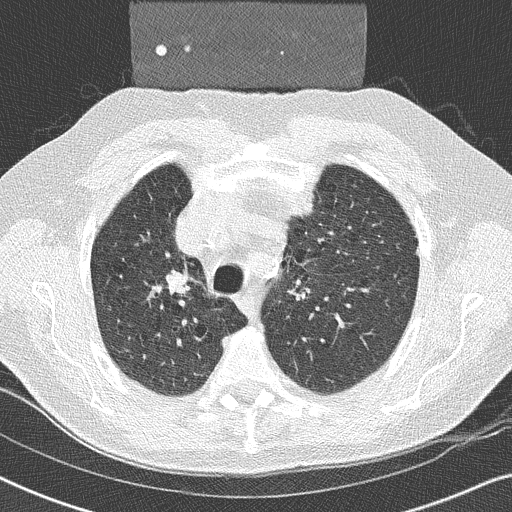
Chest CT (low-dose screening protocol), one axial image. Second annual screen. Lung window (W 1500 / L -600 HU). 2 mm slice thickness. Slice 71 of 252 in the series. Male, age 59 years at enrolment. Former smoker at enrolment.
• Expert-annotated lung lesion, bounding box [x1, y1, x2, y2] px = [151, 259, 207, 308].
• The exam's reader record, not a measurement of the box and not confirmed to be the same lesion: non-calcified nodule or mass ≥4 mm, right upper lobe, 17 × 16 mm, smooth margins, soft tissue attenuation, pre-existing on the prior screen: yes.
• Official screen result: positive, other.
• Participant outcome: lung cancer diagnosed 14 days after this screen — squamous cell carcinoma, NOS, right upper lobe, poorly differentiated (G3), stage IIA (AJCC 6th edition), 20 mm at pathology.